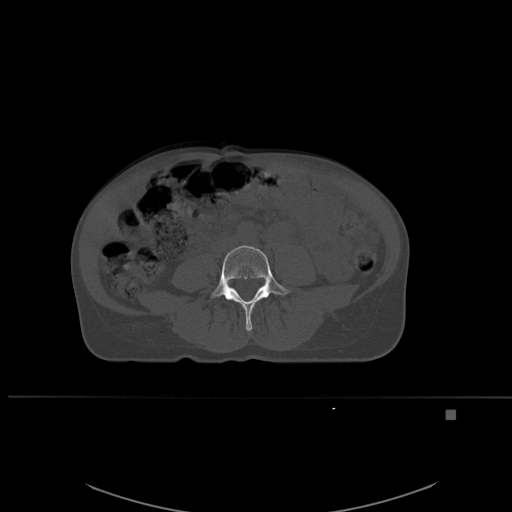
CT including the spine, one axial slice. Slice 192 of 537 in the series (ordered by position). Bone window (W 1800 / L 400 HU). 1.5 mm slice thickness. 512 × 512 image matrix, field of view 440 × 440 mm. Patient: female, 45 years. Case-level facts recorded for this patient, not image findings: primary cancer: lung.
Outlined on this slice (semi-automatically segmented with operator editing):
- L4 vertebra: bounding box [x1, y1, x2, y2] px = [210, 245, 291, 332]